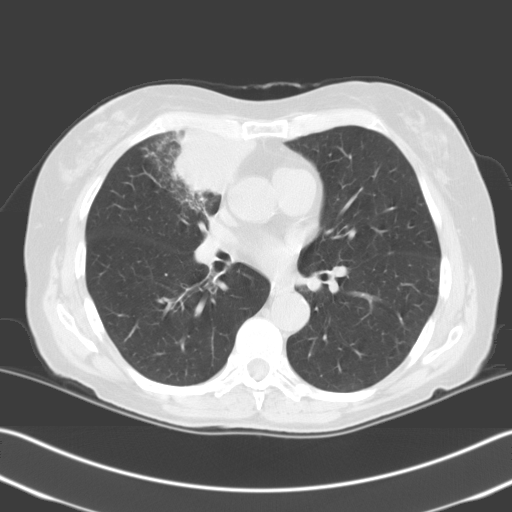
Low-dose screening chest CT, one axial slice; slice 117 of 204 in the series (ordered by position); lung window (W 1500 / L -600 HU); 3.2 mm slice thickness; 512 × 512 image matrix, field of view 348 × 348 mm.
Annotated regions visible in this slice (expert manual segmentation):
- lesion 1 (tumor, upper lobe of right lung): bounding box (x1, y1, x2, y2) in pixels: (173, 131, 254, 198)